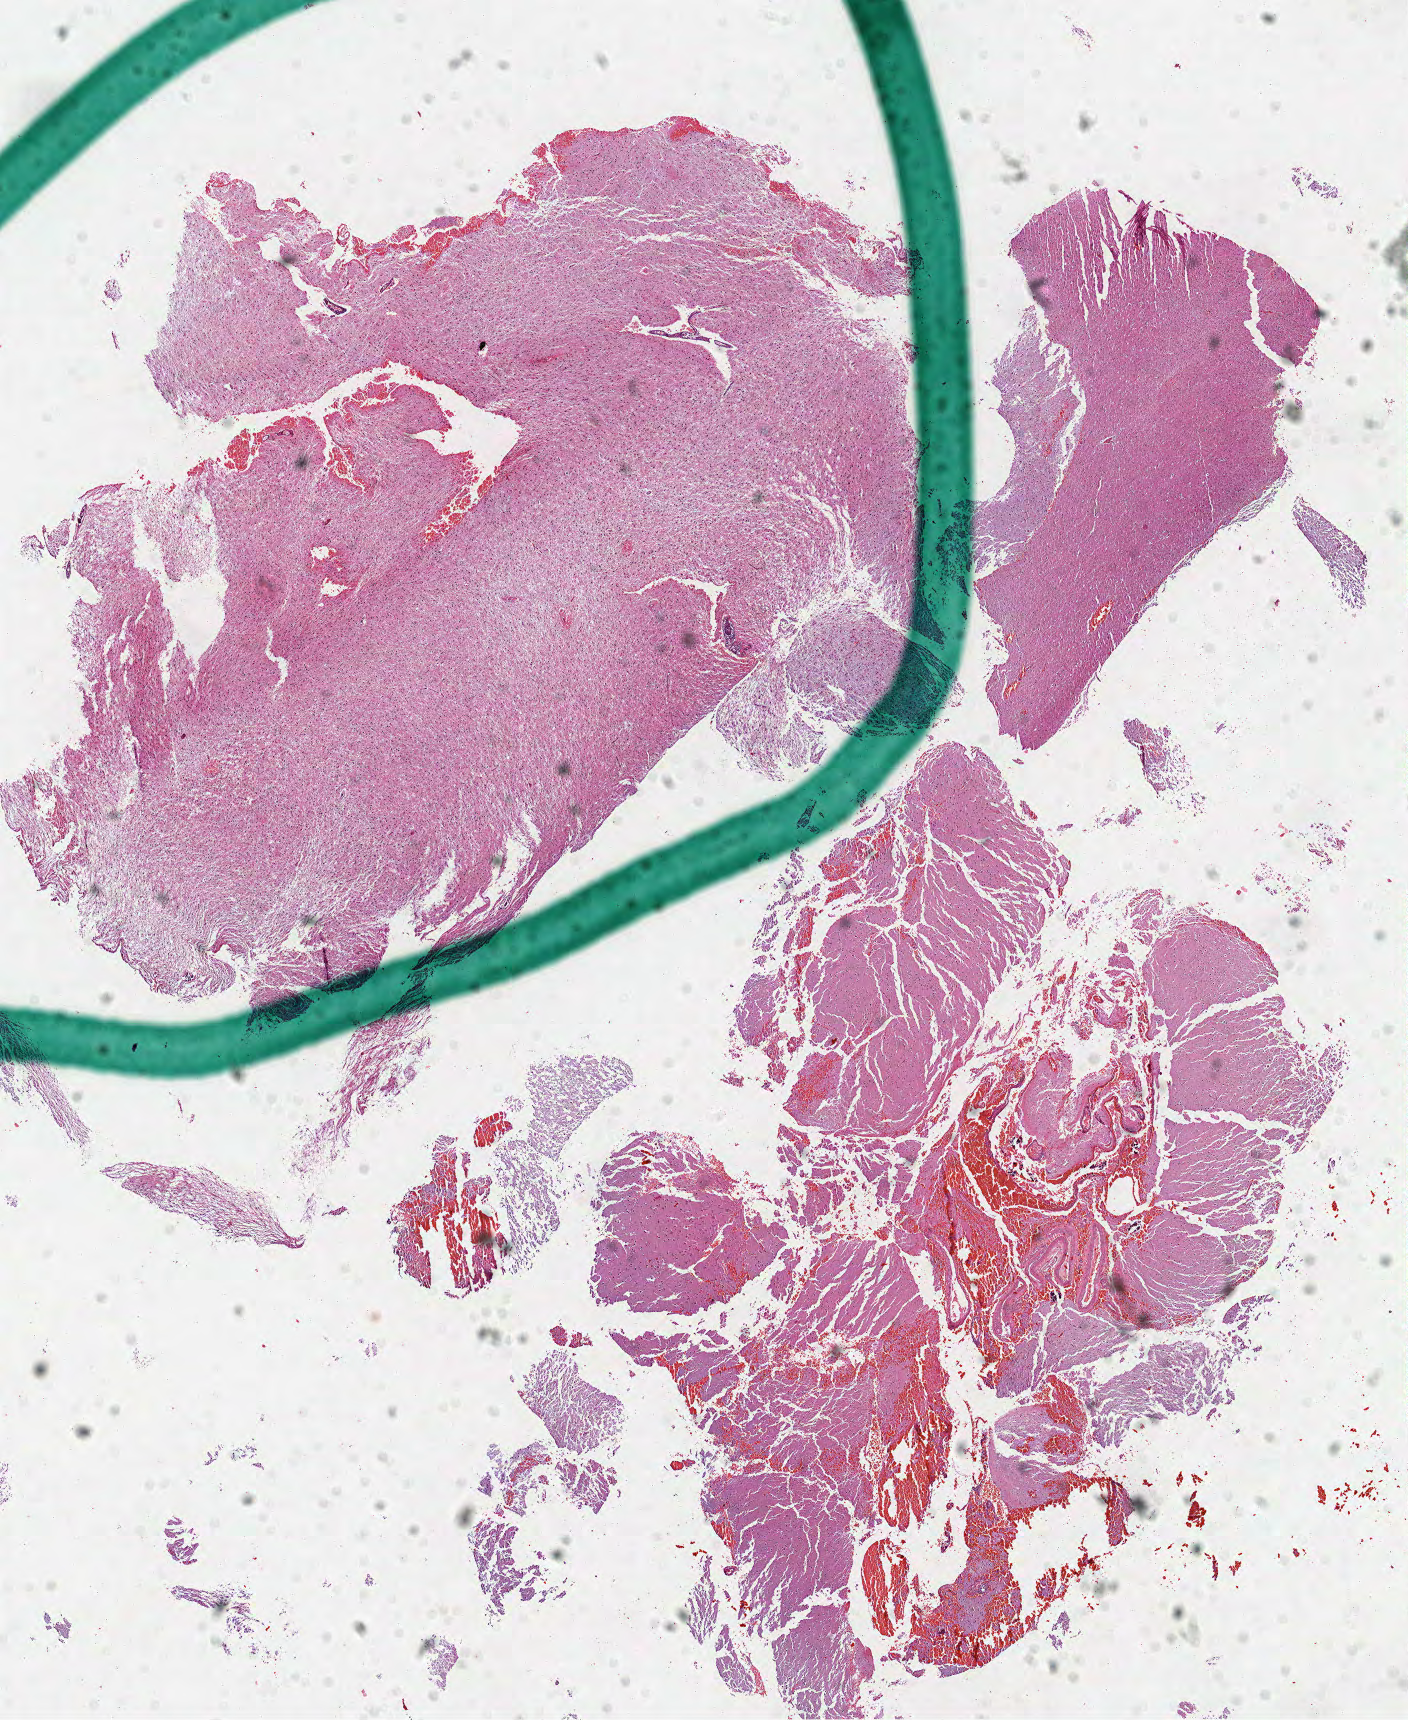
Whole-slide histology image, Hematoxylin and eosin (H&E) stained — shown as a low-resolution overview of the whole scanned area (about 11.4 x 13.9 mm). Formalin-fixed paraffin-embedded (FFPE) diagnostic section. Sample: primary tumour, brain. Female patient; age at initial diagnosis 40 years. Histologic grade: G2 (moderately differentiated).
Laterality: right. Diagnosis: Astrocytoma, NOS (cerebrum).